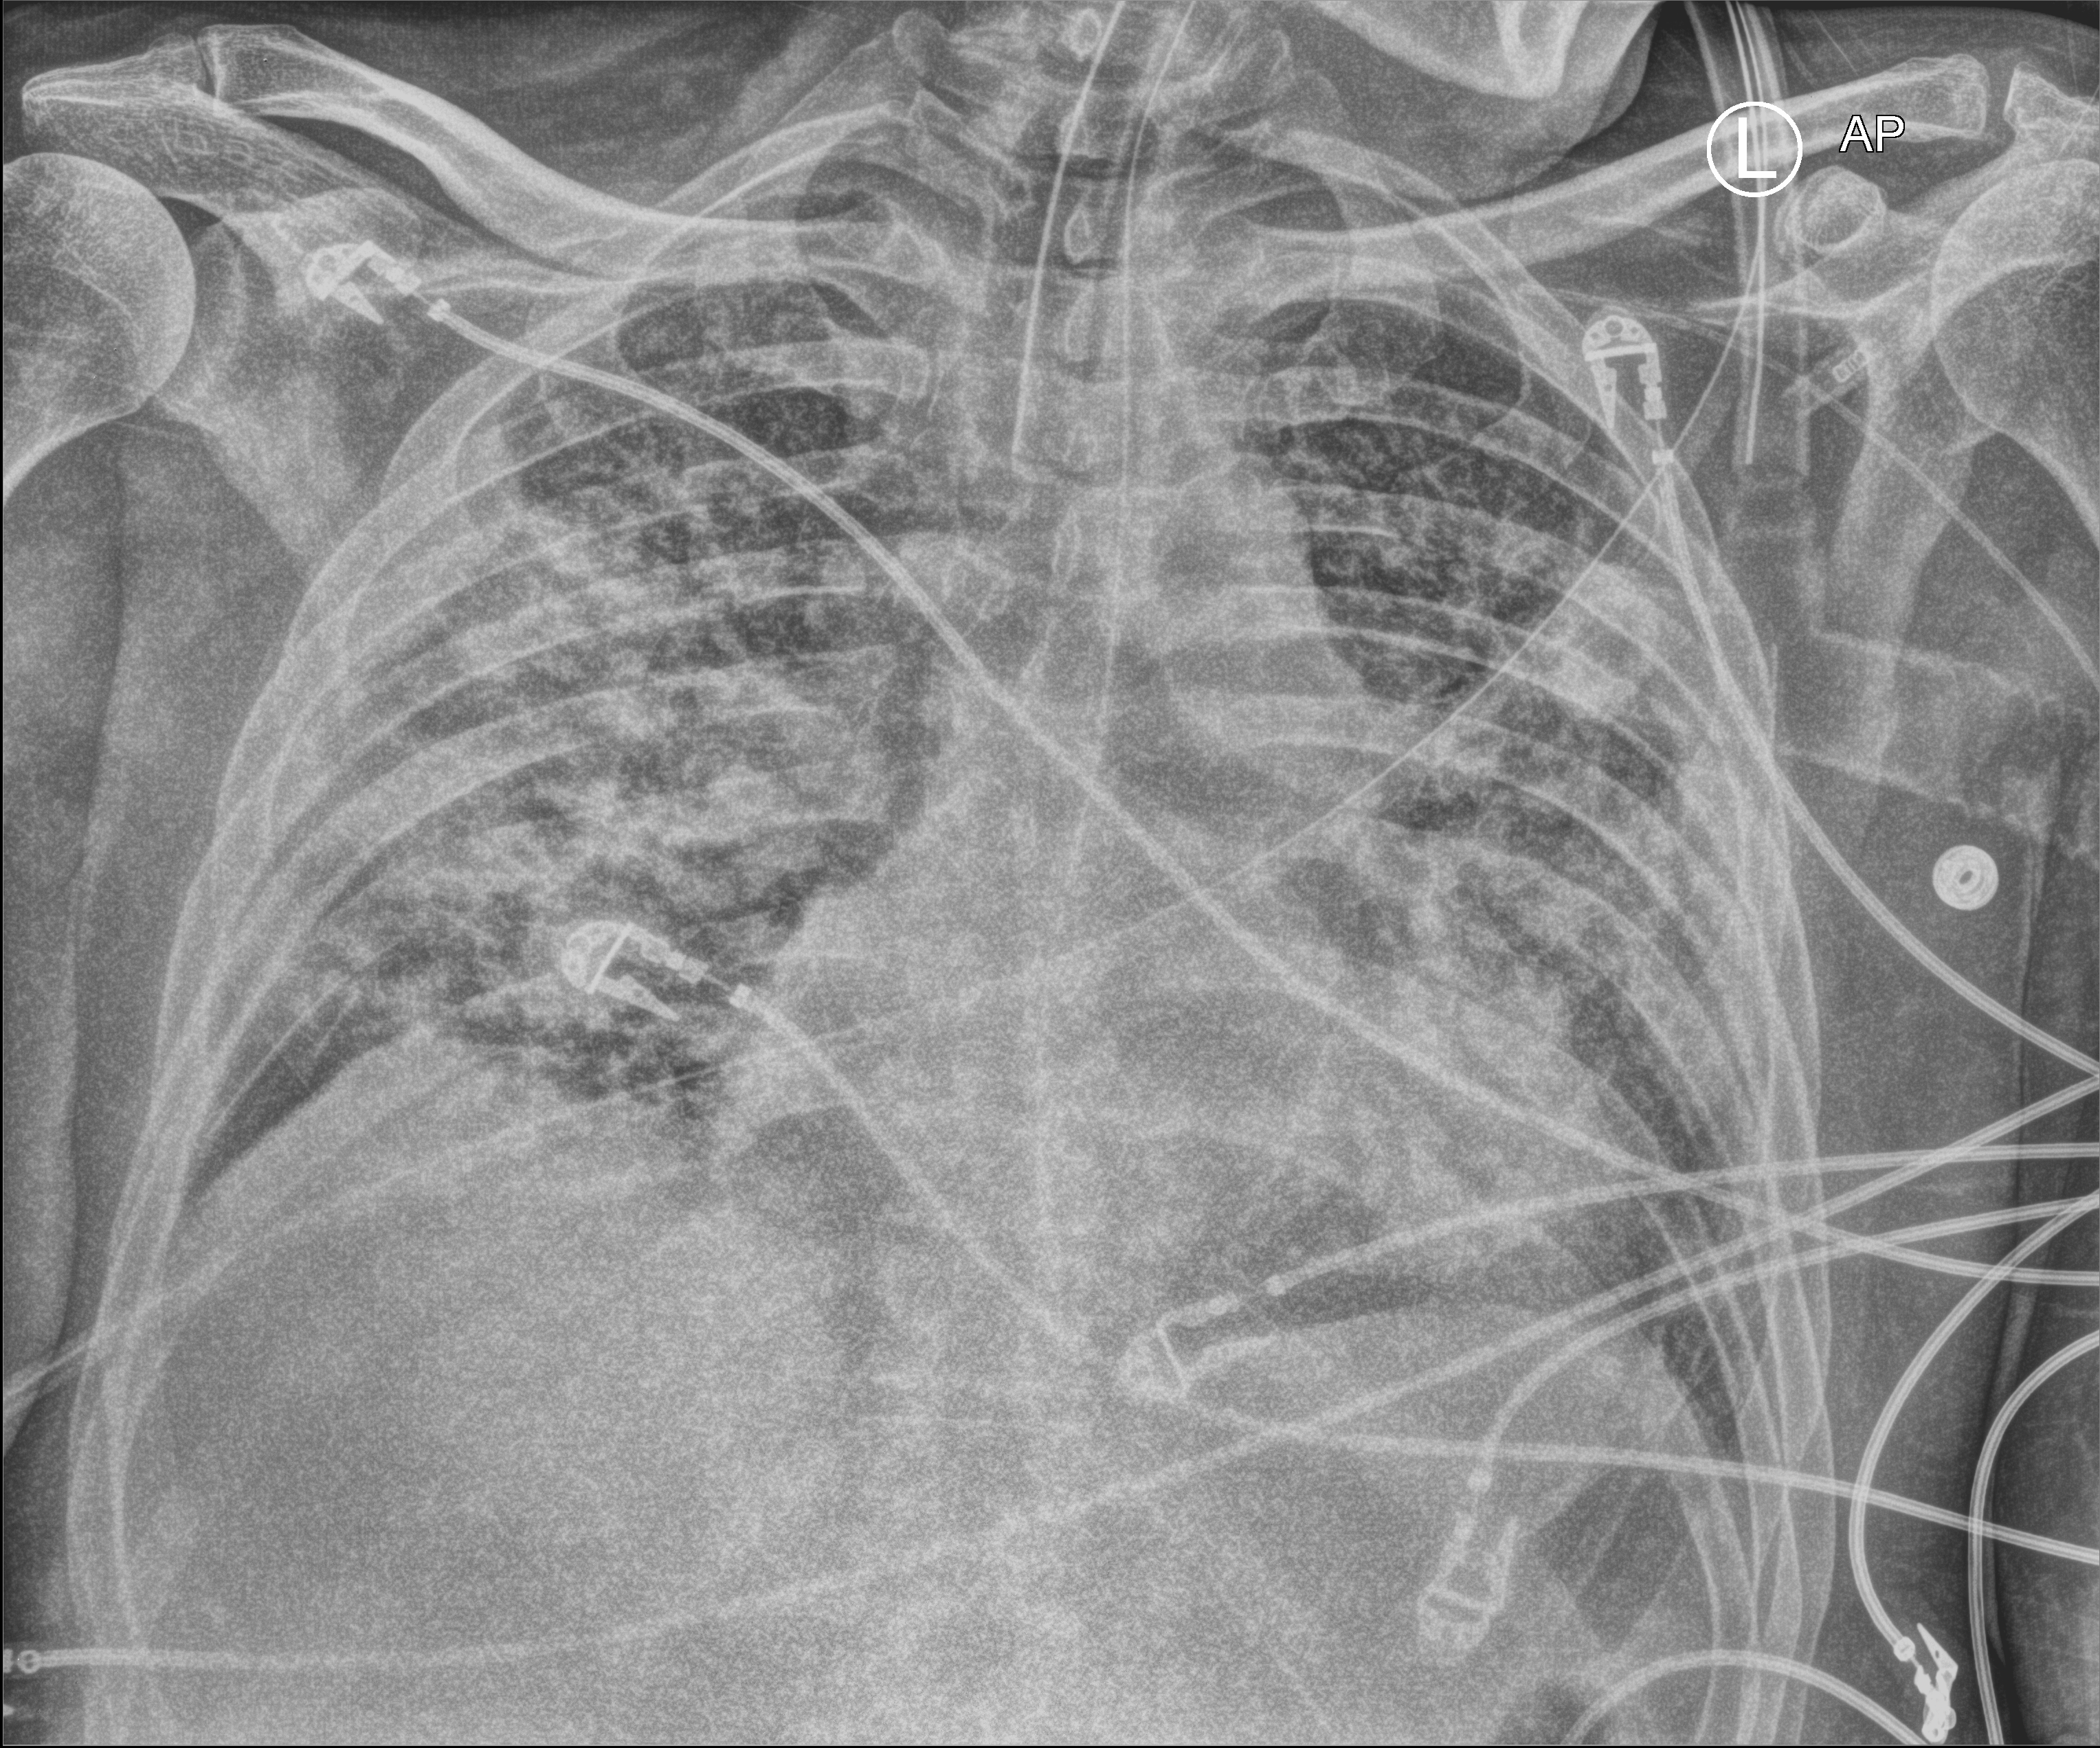
Bedside chest radiograph (computed radiography); anteroposterior (AP) projection. Male patient hospitalised with COVID-19, age 18–59 years.
Hospital-stay facts (about this admission, not read from this image; timing relative to this image not recorded):
- length of hospital stay: 75 days
- admitted to intensive care during this hospital stay: yes